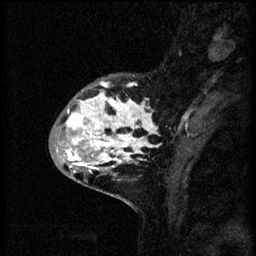
Breast MRI (dynamic contrast-enhanced), one sagittal slice; position 17 of 60 along the scan axis; 3 images stored at this slice position (order not interpretable as contrast timing); 1.5 T; TE 4.2 ms, TR 8.2 ms; 2 mm slice thickness; 256 × 256 image matrix, field of view 180 × 180 mm. Patient: female, 41 years.
Annotated regions visible in this slice (semi-automatic segmentation, software-assisted and operator-edited):
- analysis volume of interest (the breast-tissue region the enhancement analysis was run in; not a lesion): bounding box [x1, y1, x2, y2] px = [53, 74, 160, 175]
- tumour enhancement mask (voxels above the 70 % enhancement threshold inside the analysis volume of interest): [64, 82, 160, 173]